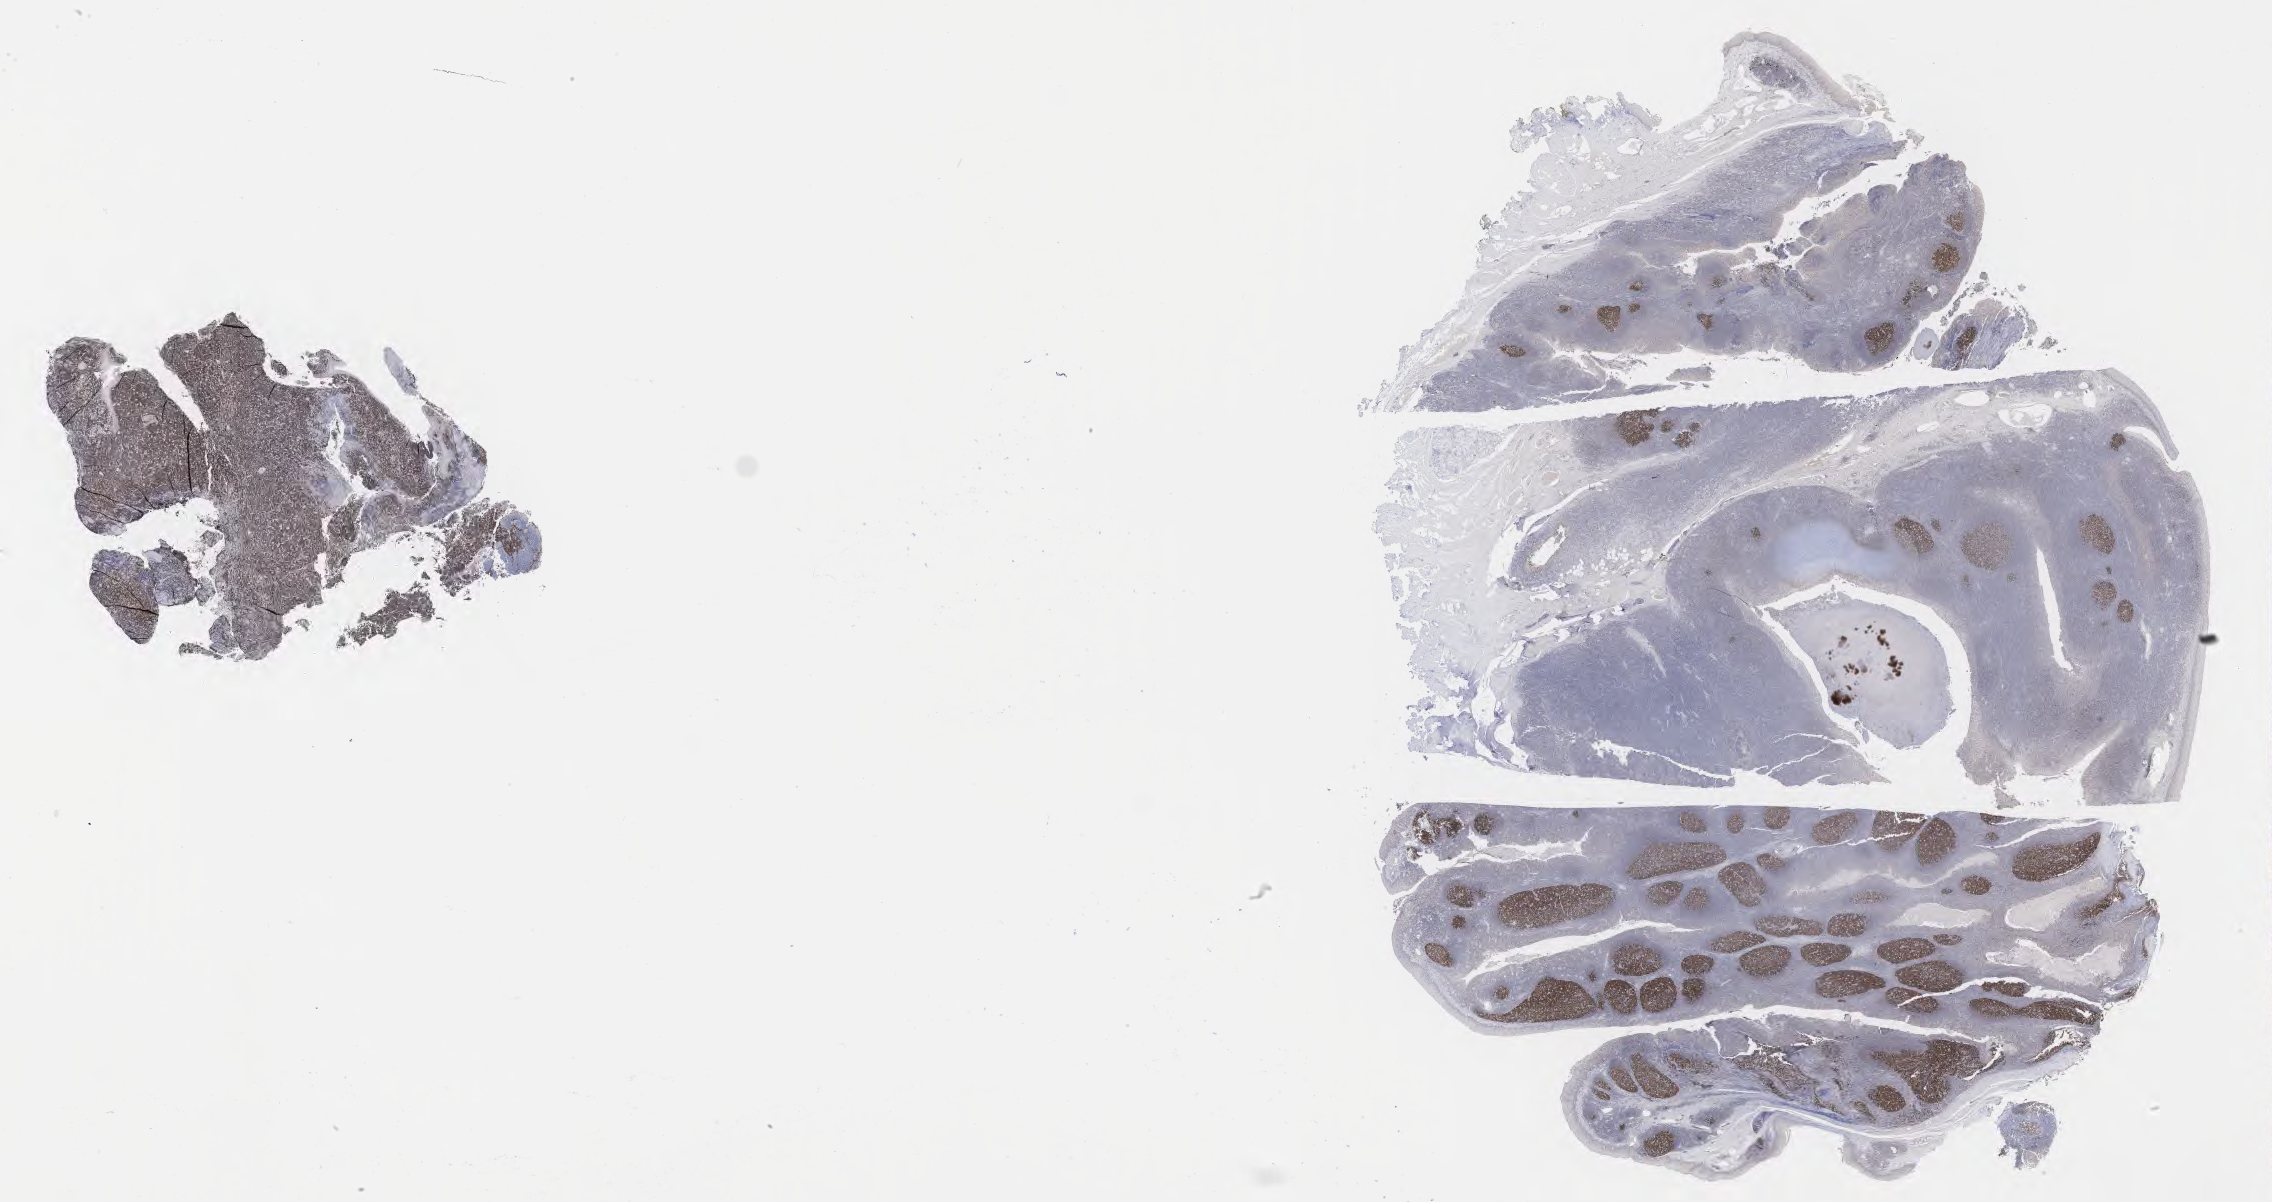
Immunohistochemistry (IHC) whole-slide image stained for BCL6, whole scanned area (about 36.7 x 19.4 mm) shown as a low-resolution overview. Specimen: tumor tissue. Male patient; age at initial diagnosis 3 years.
• histologic diagnosis: Burkitt lymphoma, NOS